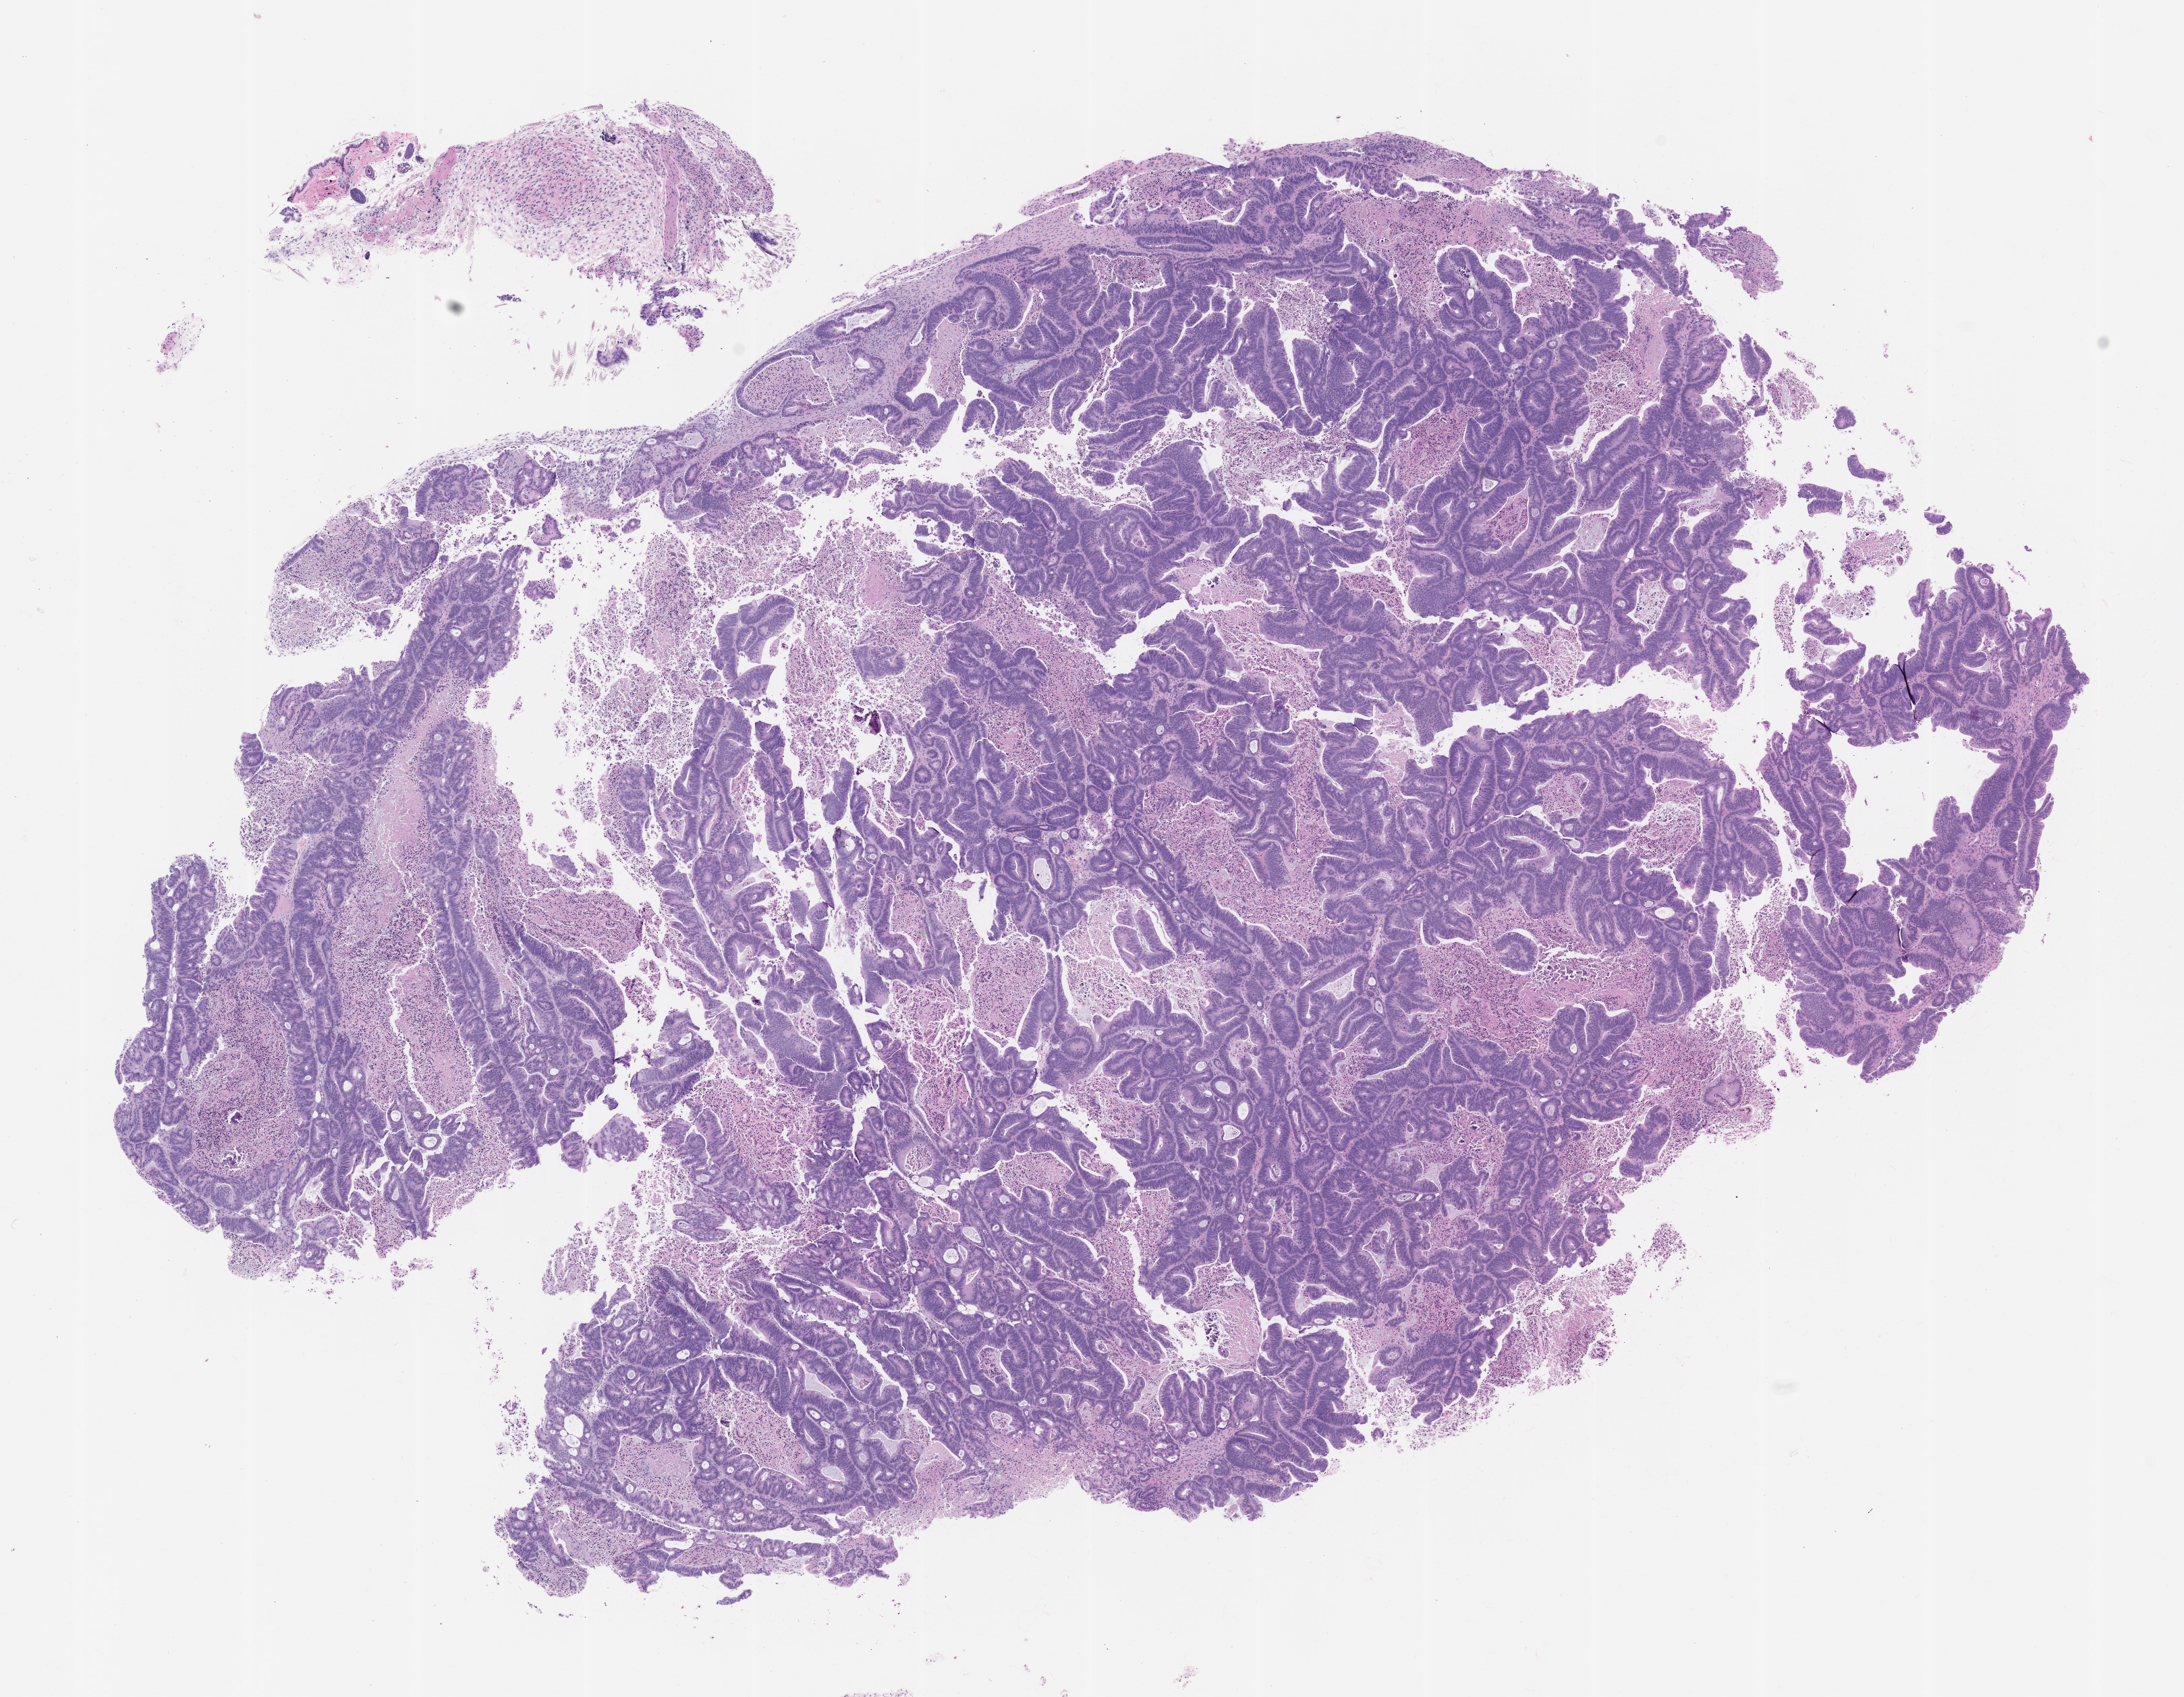
H&E whole-slide image of a patient-derived xenograft (PDX) tumor grown in a mouse, passage 2, a low-resolution overview of the entire scanned area, about 13.0 x 10.1 mm. Formalin-fixed paraffin-embedded section. Tumor site category: colon.
Originating patient diagnosis: Colon Adenocarcinoma.